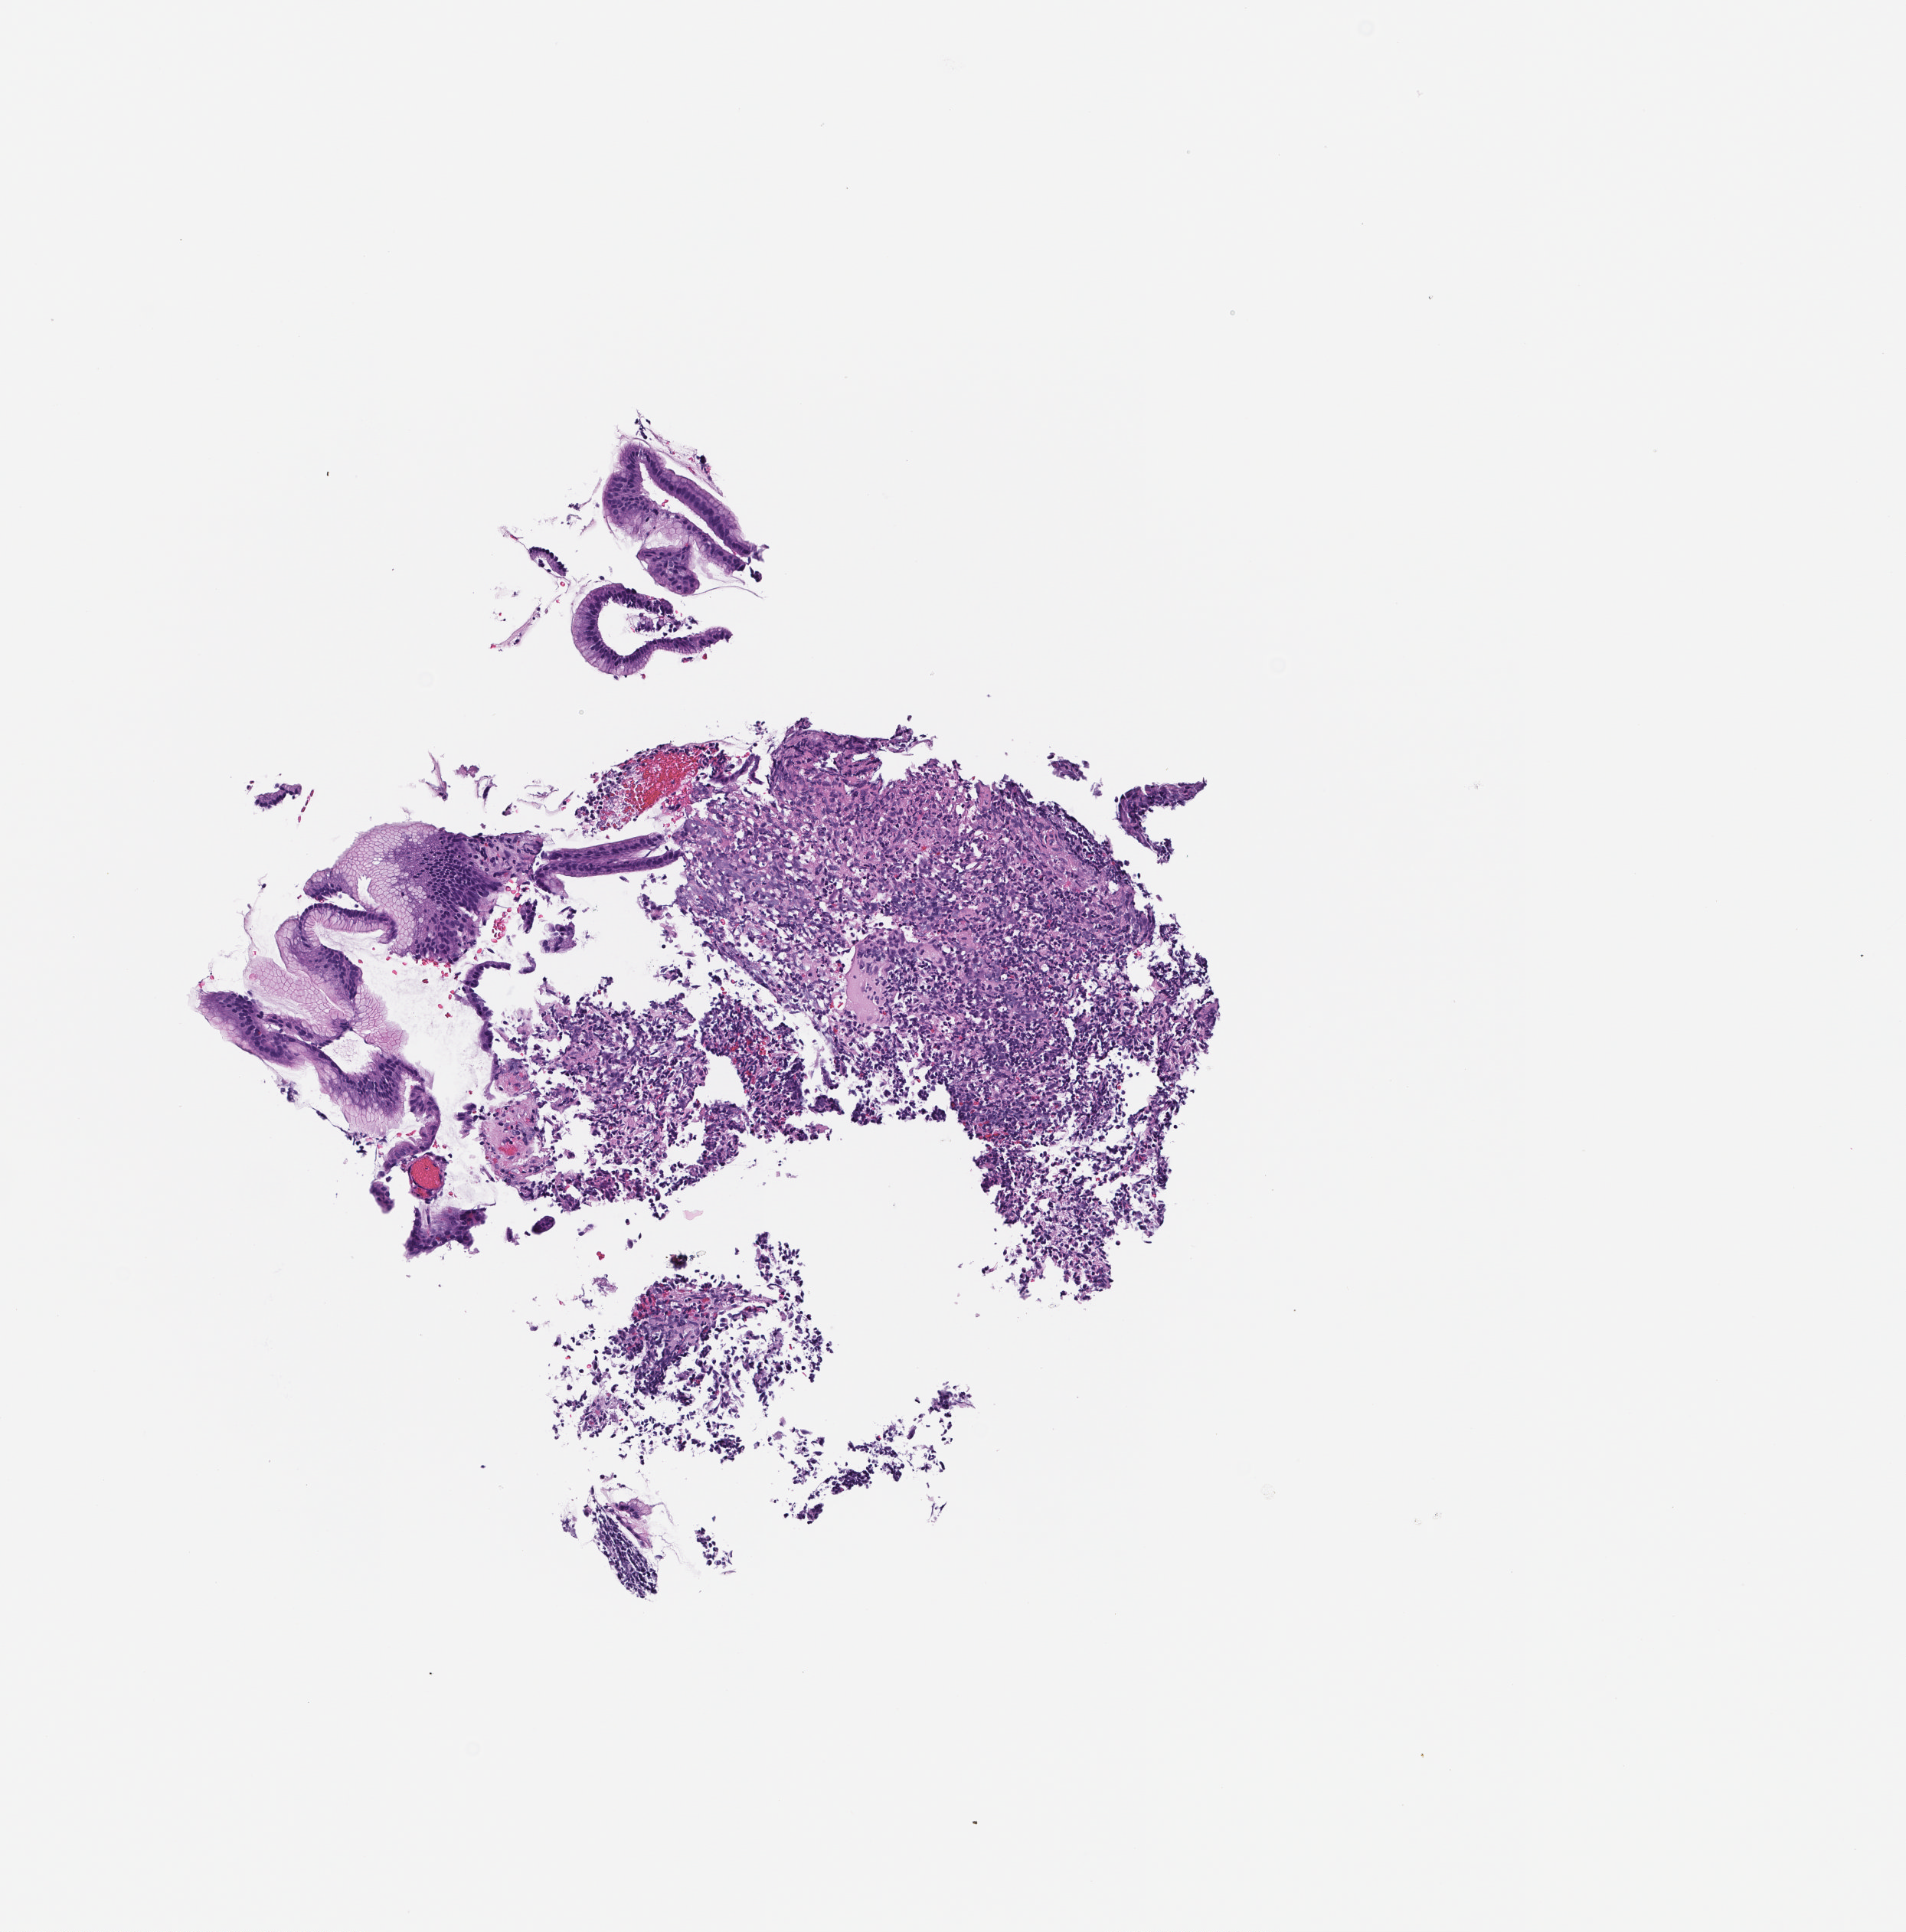
Whole-slide image, haematoxylin and eosin stain — low-resolution overview of the scanned area, about 2.5 x 2.5 mm, formalin-fixed paraffin-embedded section, tissue site: stomach, specimen time point: archival tissue. Patient: female.
This section: primary tumor. Diagnosis: Adenocarcinoma of the Gastroesophageal Junction.